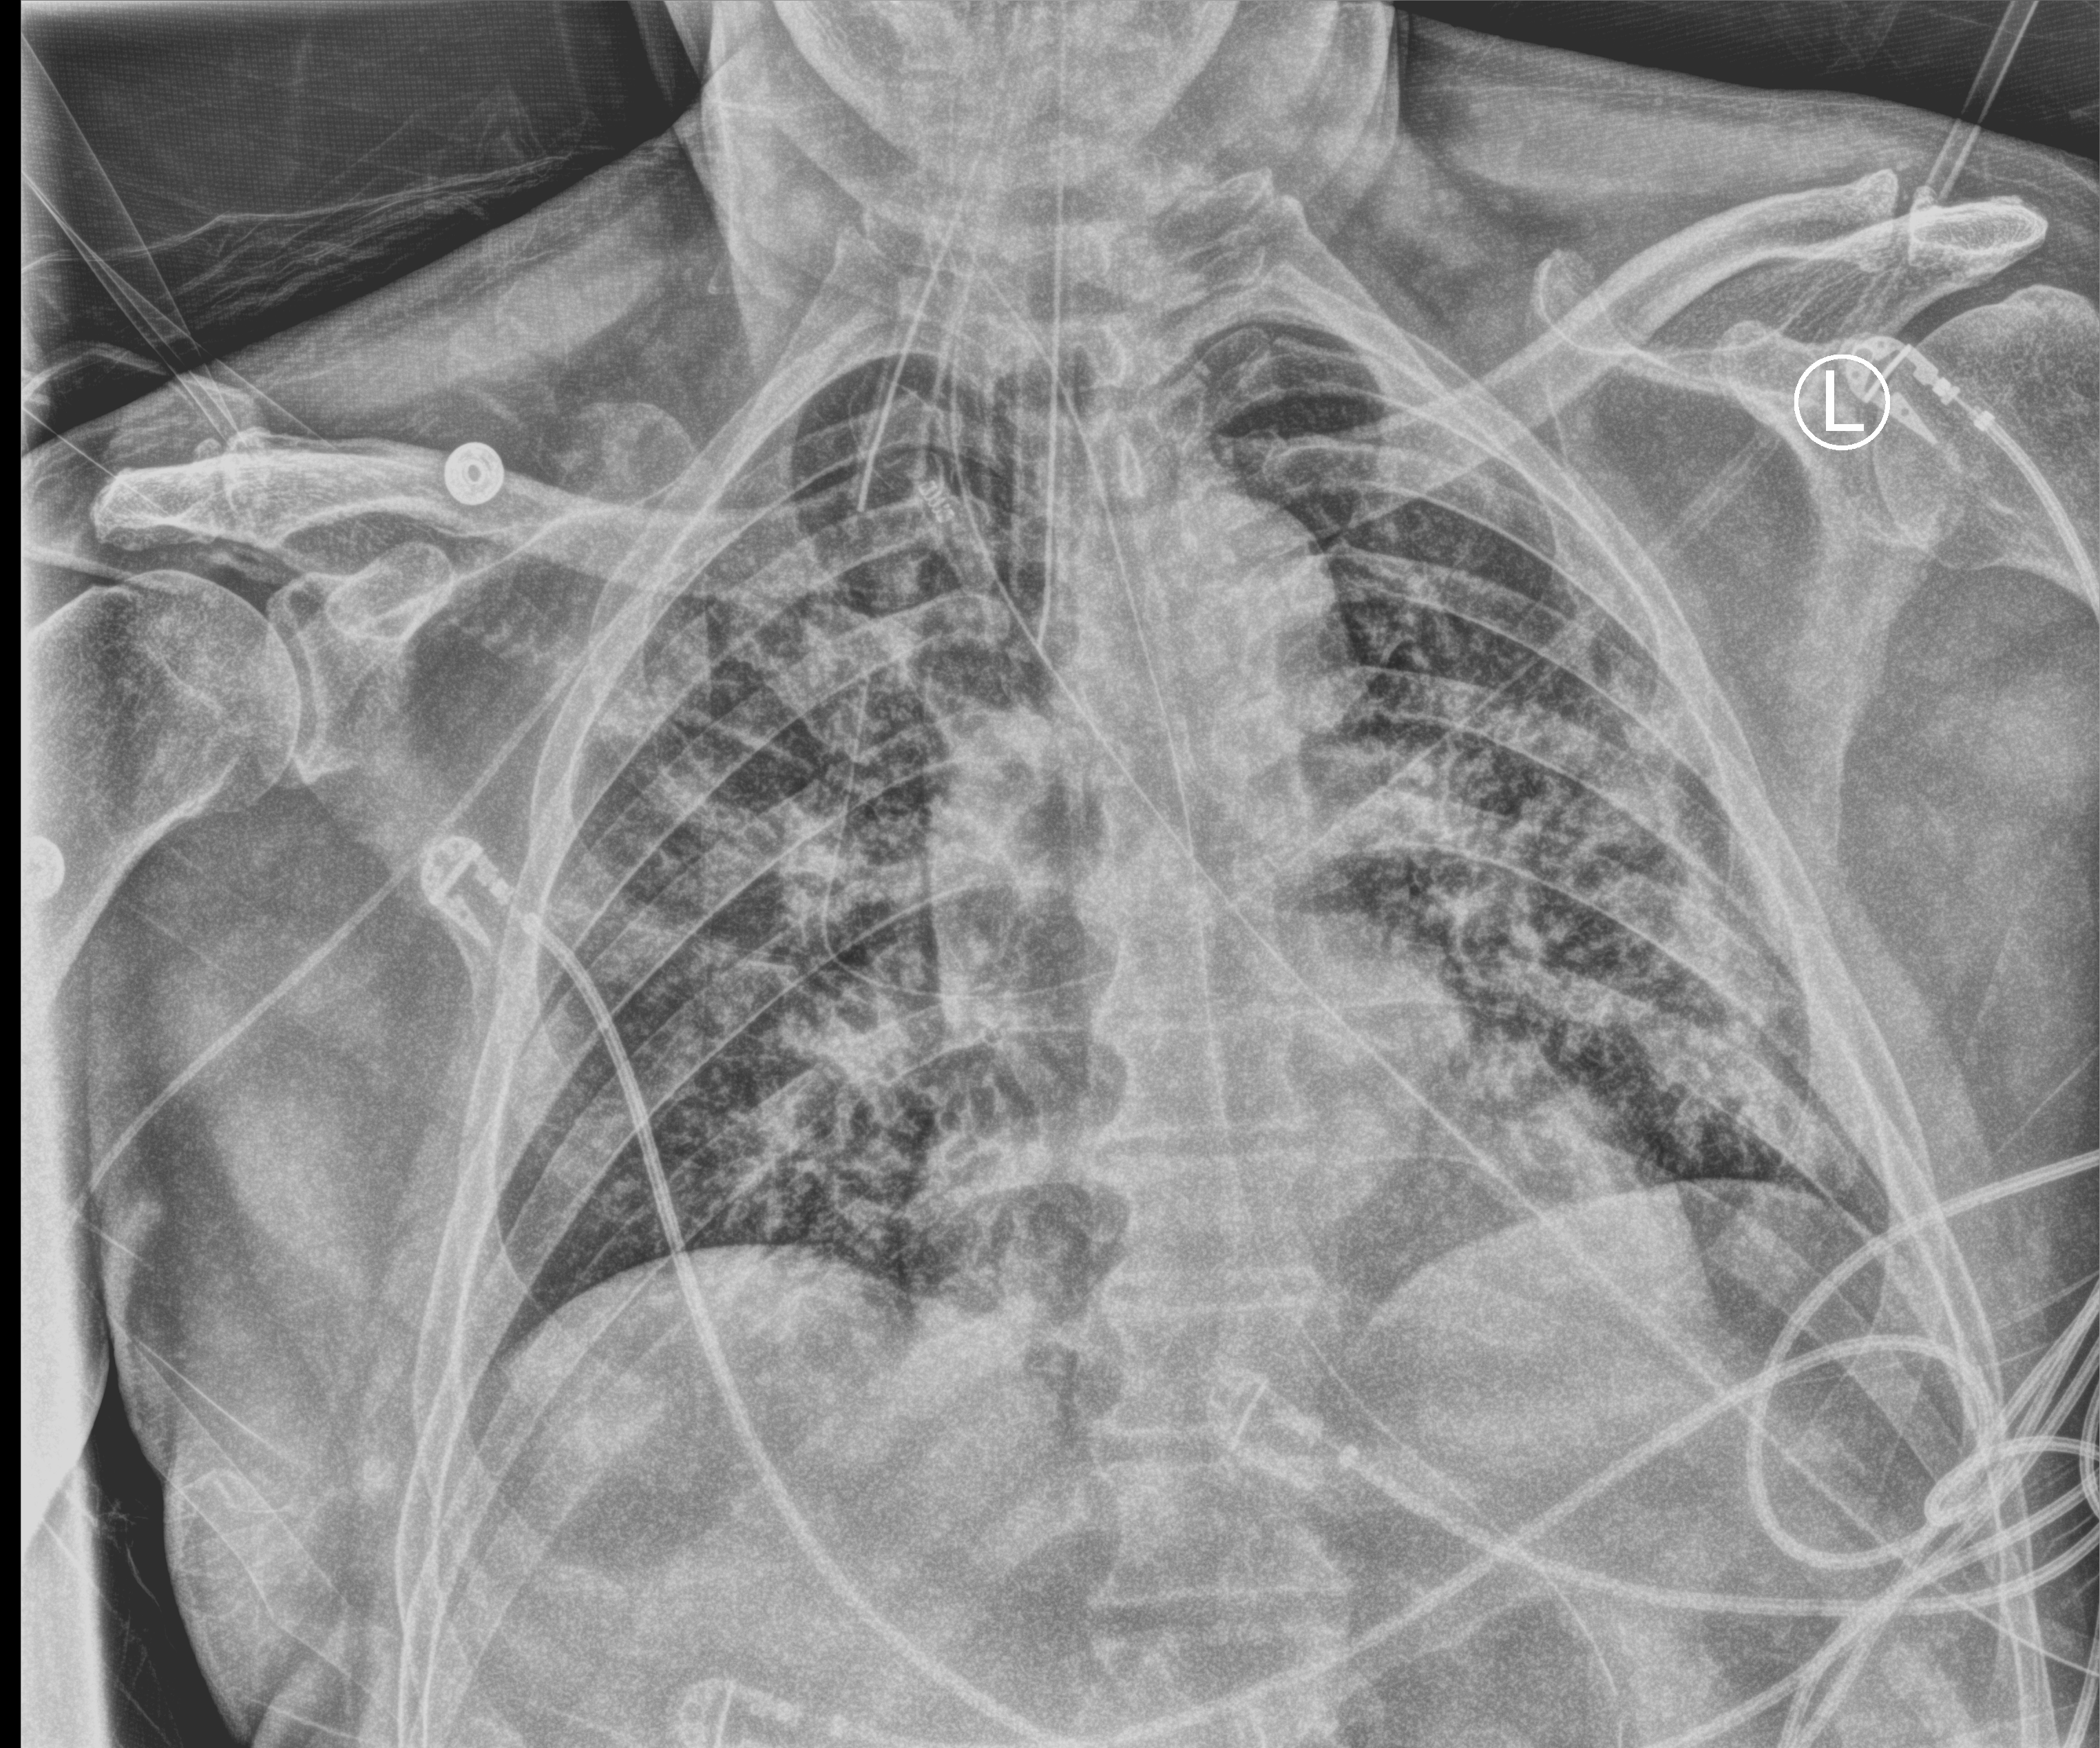
Chest X-ray (portable), anteroposterior (AP) projection. Patient hospitalised with COVID-19; male, aged 60–74 years.
Admission-level facts for this patient (not findings on this image; timing relative to this image not recorded):
- diabetes (admission record): no